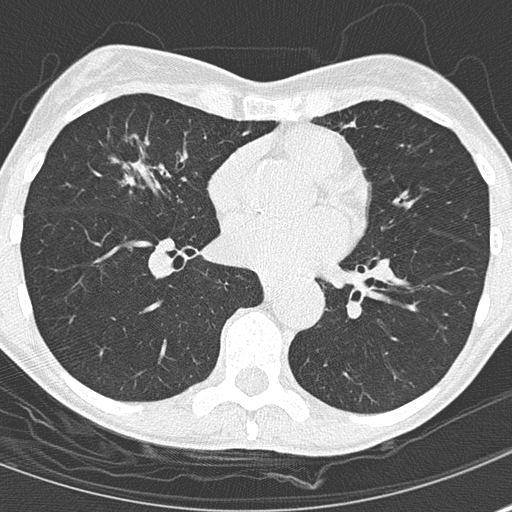
Low-dose screening chest CT, axial slice, second screening round (one year after baseline), lung window (W 1500 / L -600 HU), 2 mm slice thickness, 120 kVp, 512 × 512 image matrix, field of view 280 × 280 mm. Female, age 67 years at enrolment.
• Expert reader's lesion annotation, bounding box <82,120,182,210> (left, top, right, bottom; pixels).
• The screening reader recorded 2 non-calcified nodules or masses ≥4 mm on this exam (right middle lobe, right middle lobe); which of them this box marks is not recorded.
• Later outcome: lung cancer diagnosed 475 days after this screen — bronchiolo-alveolar adenocarcinoma, NOS, right middle lobe, well differentiated (G1), stage IA (AJCC 6th edition), 25 mm at pathology.